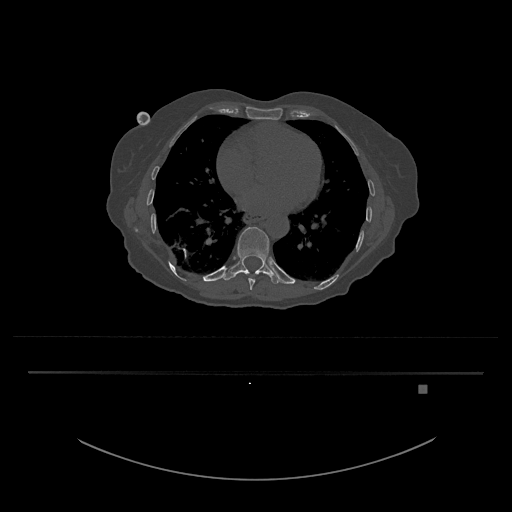
CT including the spine, one axial slice; slice 729 of 797 in the series (ordered by position); 120 kVp; bone window (W 1800 / L 400 HU); 0.5 mm slice thickness; 512 × 512 image matrix, field of view 500 × 500 mm. Patient: female, 57 years. From the clinical record (not read from this slice): primary cancer: cervical.
Structures marked on this image (semi-automatic segmentation, software-assisted and operator-edited):
- T10 vertebra: bounding box (x1, y1, x2, y2) in pixels: (222, 227, 282, 284)
- T9 vertebra: (248, 278, 255, 290)